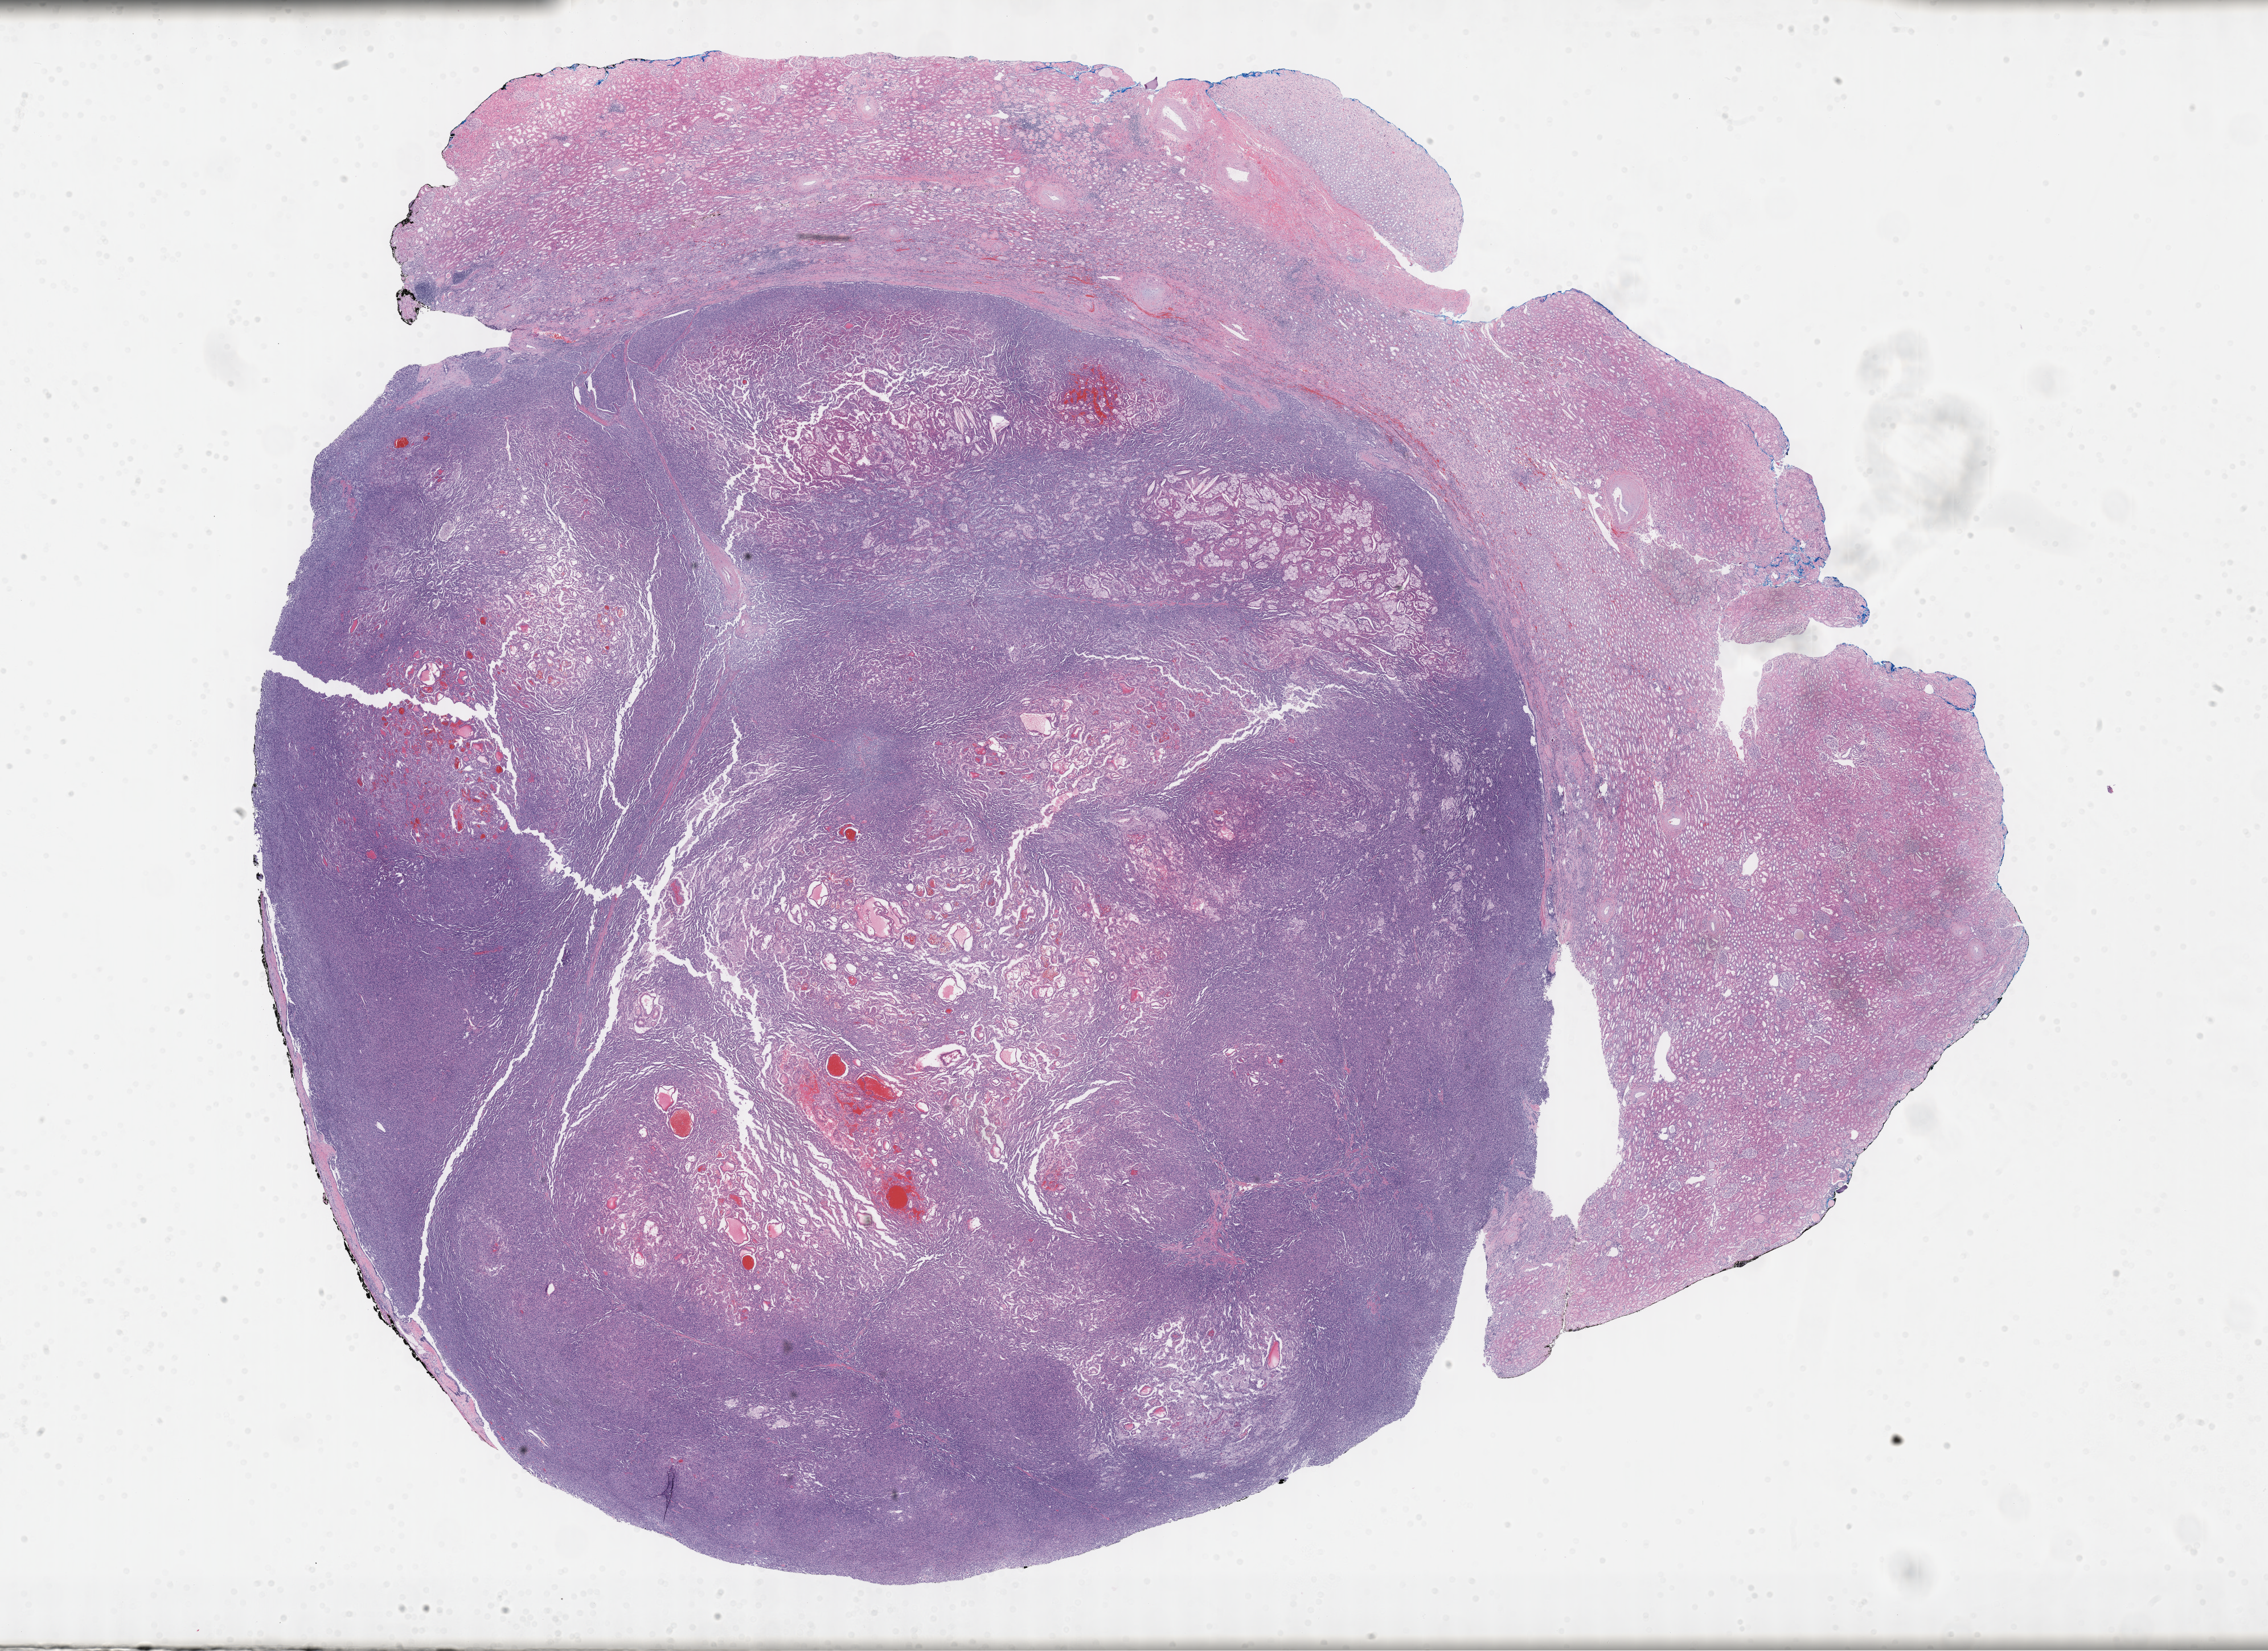
Whole-slide histology image, H&E-stained — low-resolution overview of the scanned area, about 32.2 x 23.5 mm, FFPE section, primary tumour sample from the kidney. Male, age 57 years at initial diagnosis.
AJCC pathologic stage: I (7th edition). Diagnosis: Papillary adenocarcinoma, NOS.